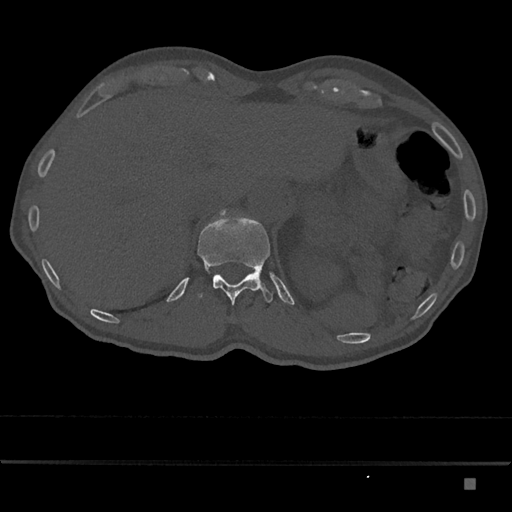
CT including the spine, one axial slice; slice 610 of 797 in the series (ordered by position); reconstruction kernel Br40s/3; 120 kVp; bone window (W 1800 / L 400 HU); 0.5 mm slice thickness; 512 × 512 image matrix, field of view 390 × 390 mm. Male patient, age 72 years. From the clinical record (not read from this slice): primary cancer: prostate.
Structures marked on this image (semi-automatically segmented with operator editing):
- T12 vertebra: bounding box <197,213,274,305> (left, top, right, bottom; pixels)